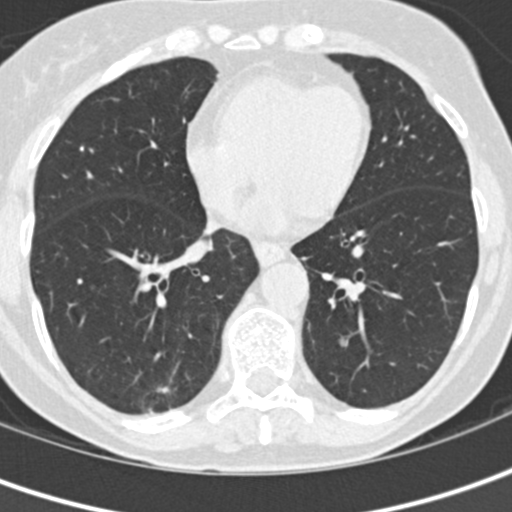
Low-dose screening chest CT, one axial slice; slice 58 of 152 in the series (ordered by position); 120 kVp; lung window (W 1500 / L -600 HU); 2 mm slice thickness; 512 × 512 image matrix.
Structures marked on this image (manually delineated by an expert):
- lesion 1 (tumor, lower lobe of right lung): bounding box (x1, y1, x2, y2) in pixels: (157, 387, 170, 393)